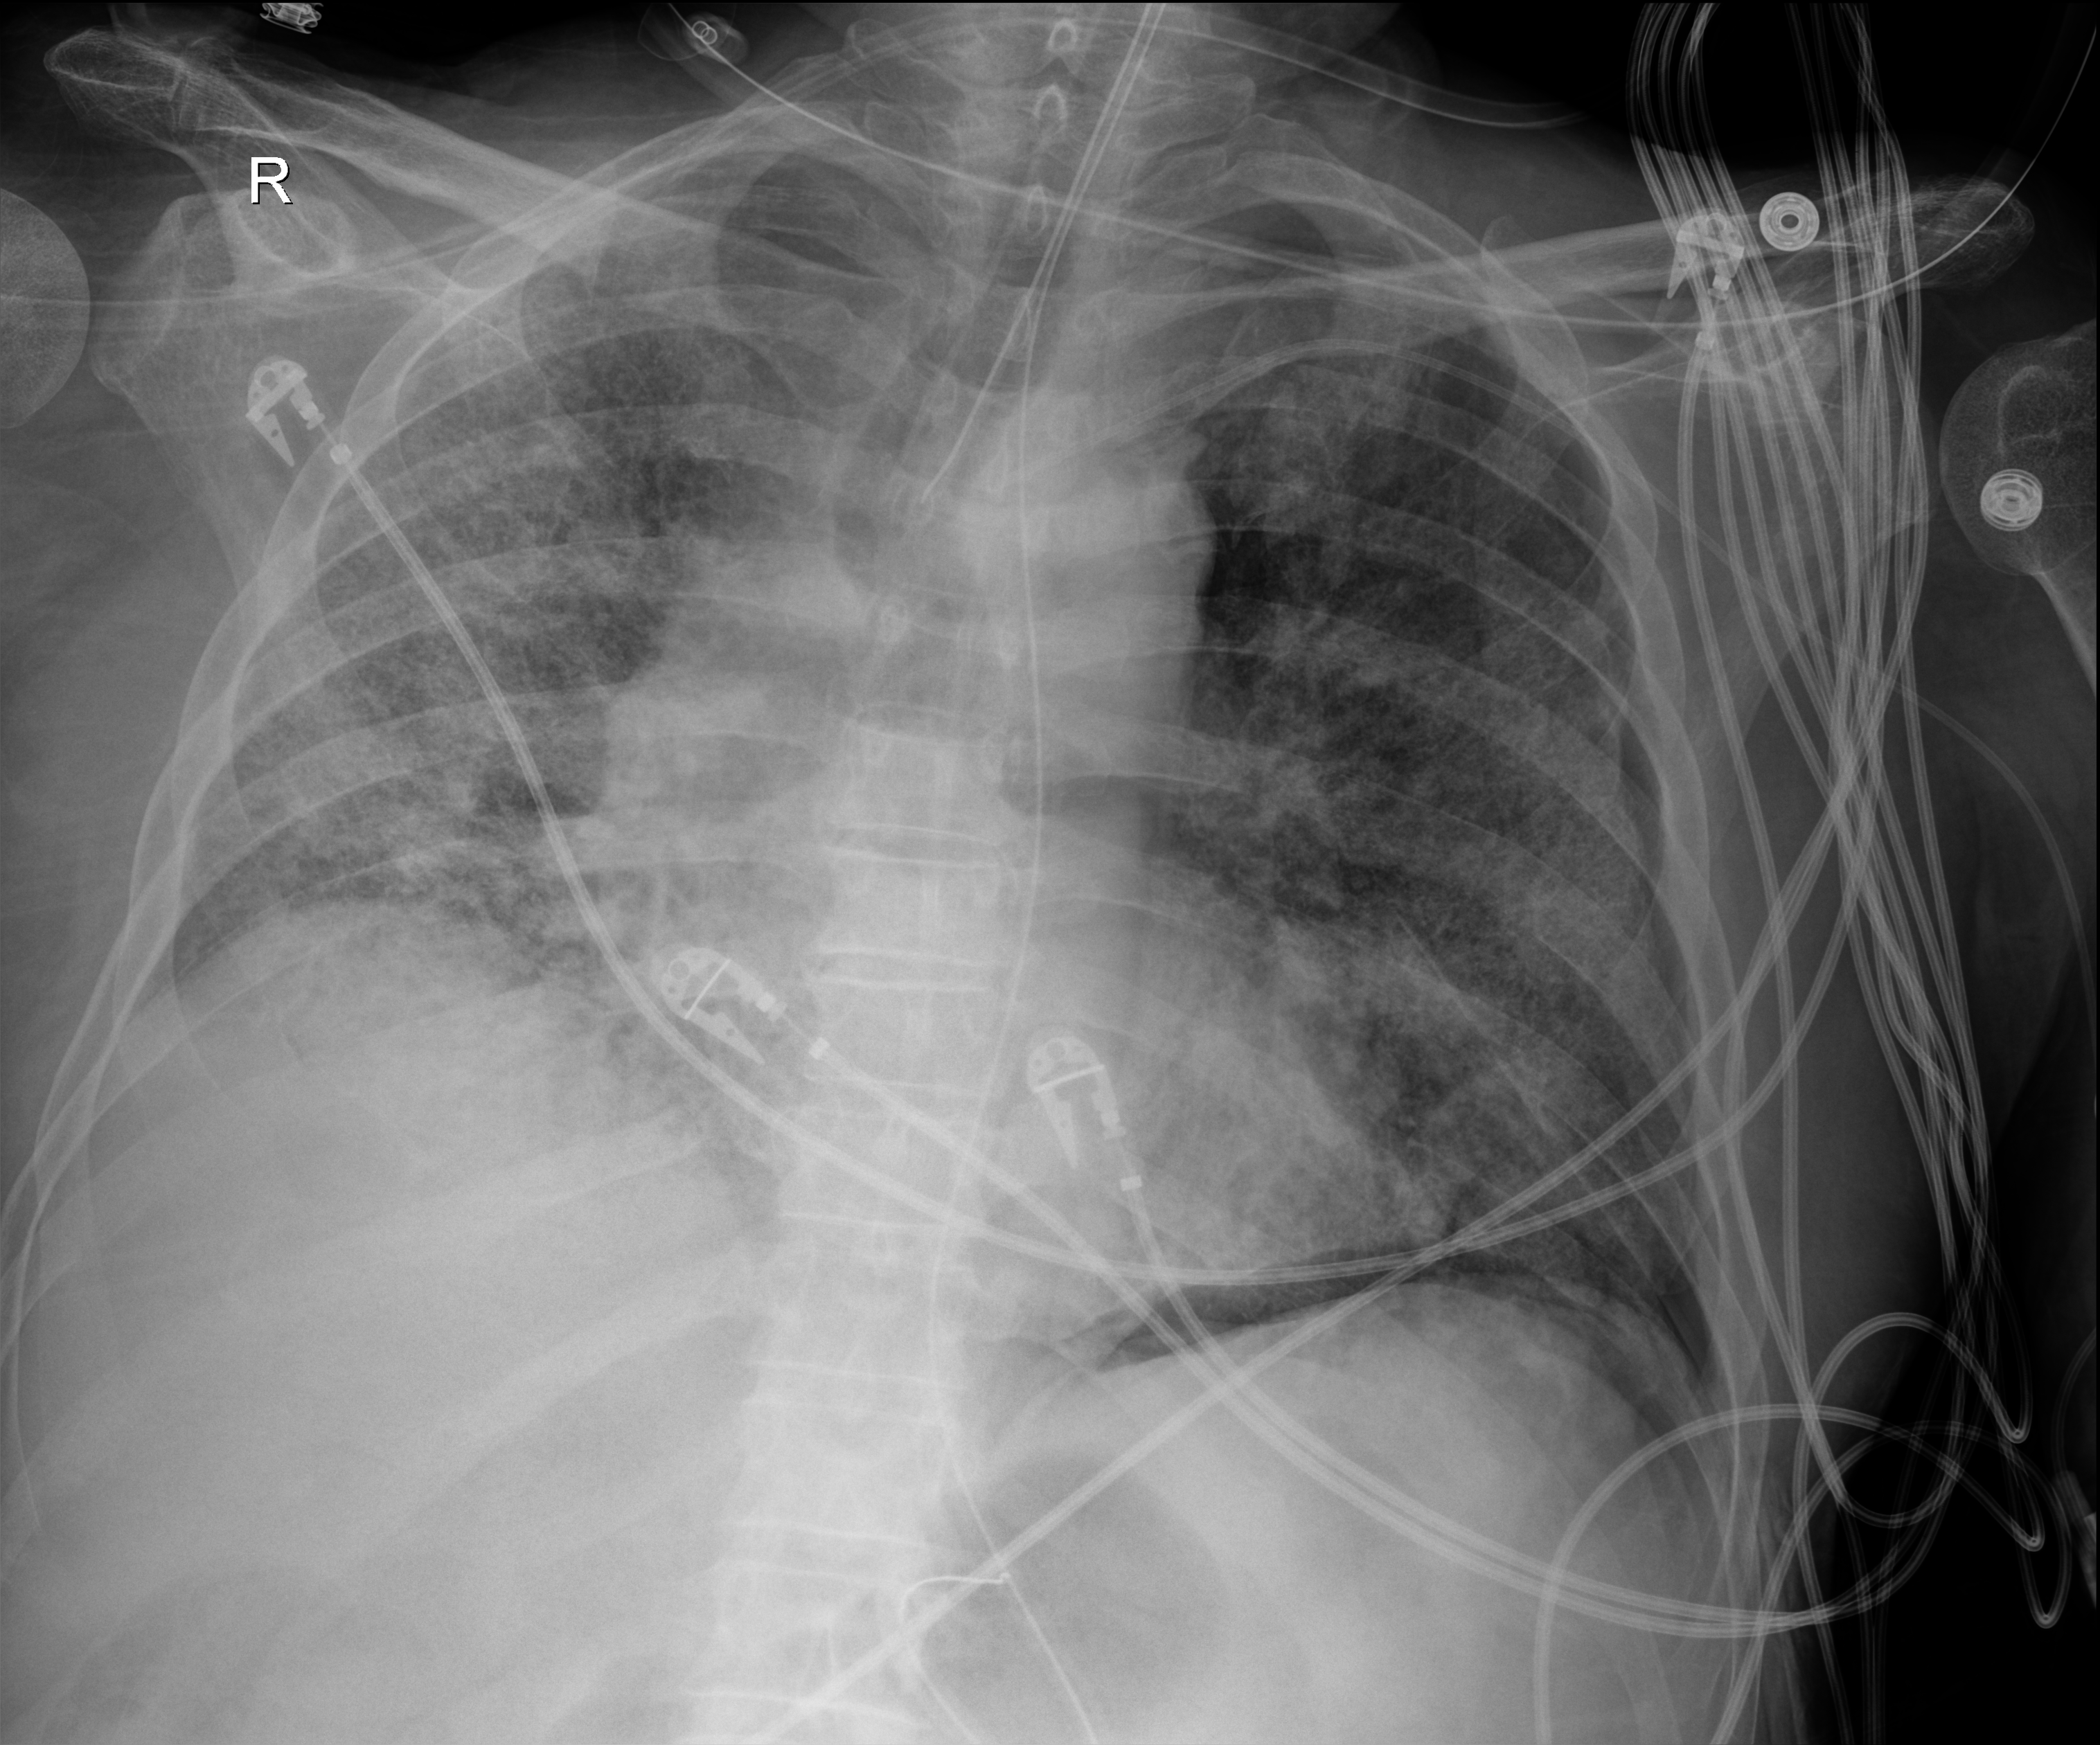
Chest radiograph, anteroposterior (AP) projection. Patient hospitalised with COVID-19; male, aged 60–74 years.
Hospital-stay facts (about this admission, not read from this image; timing relative to this image not recorded):
- mechanically ventilated during this hospital stay: yes
- length of hospital stay: 54 days
- admitted to intensive care during this hospital stay: yes